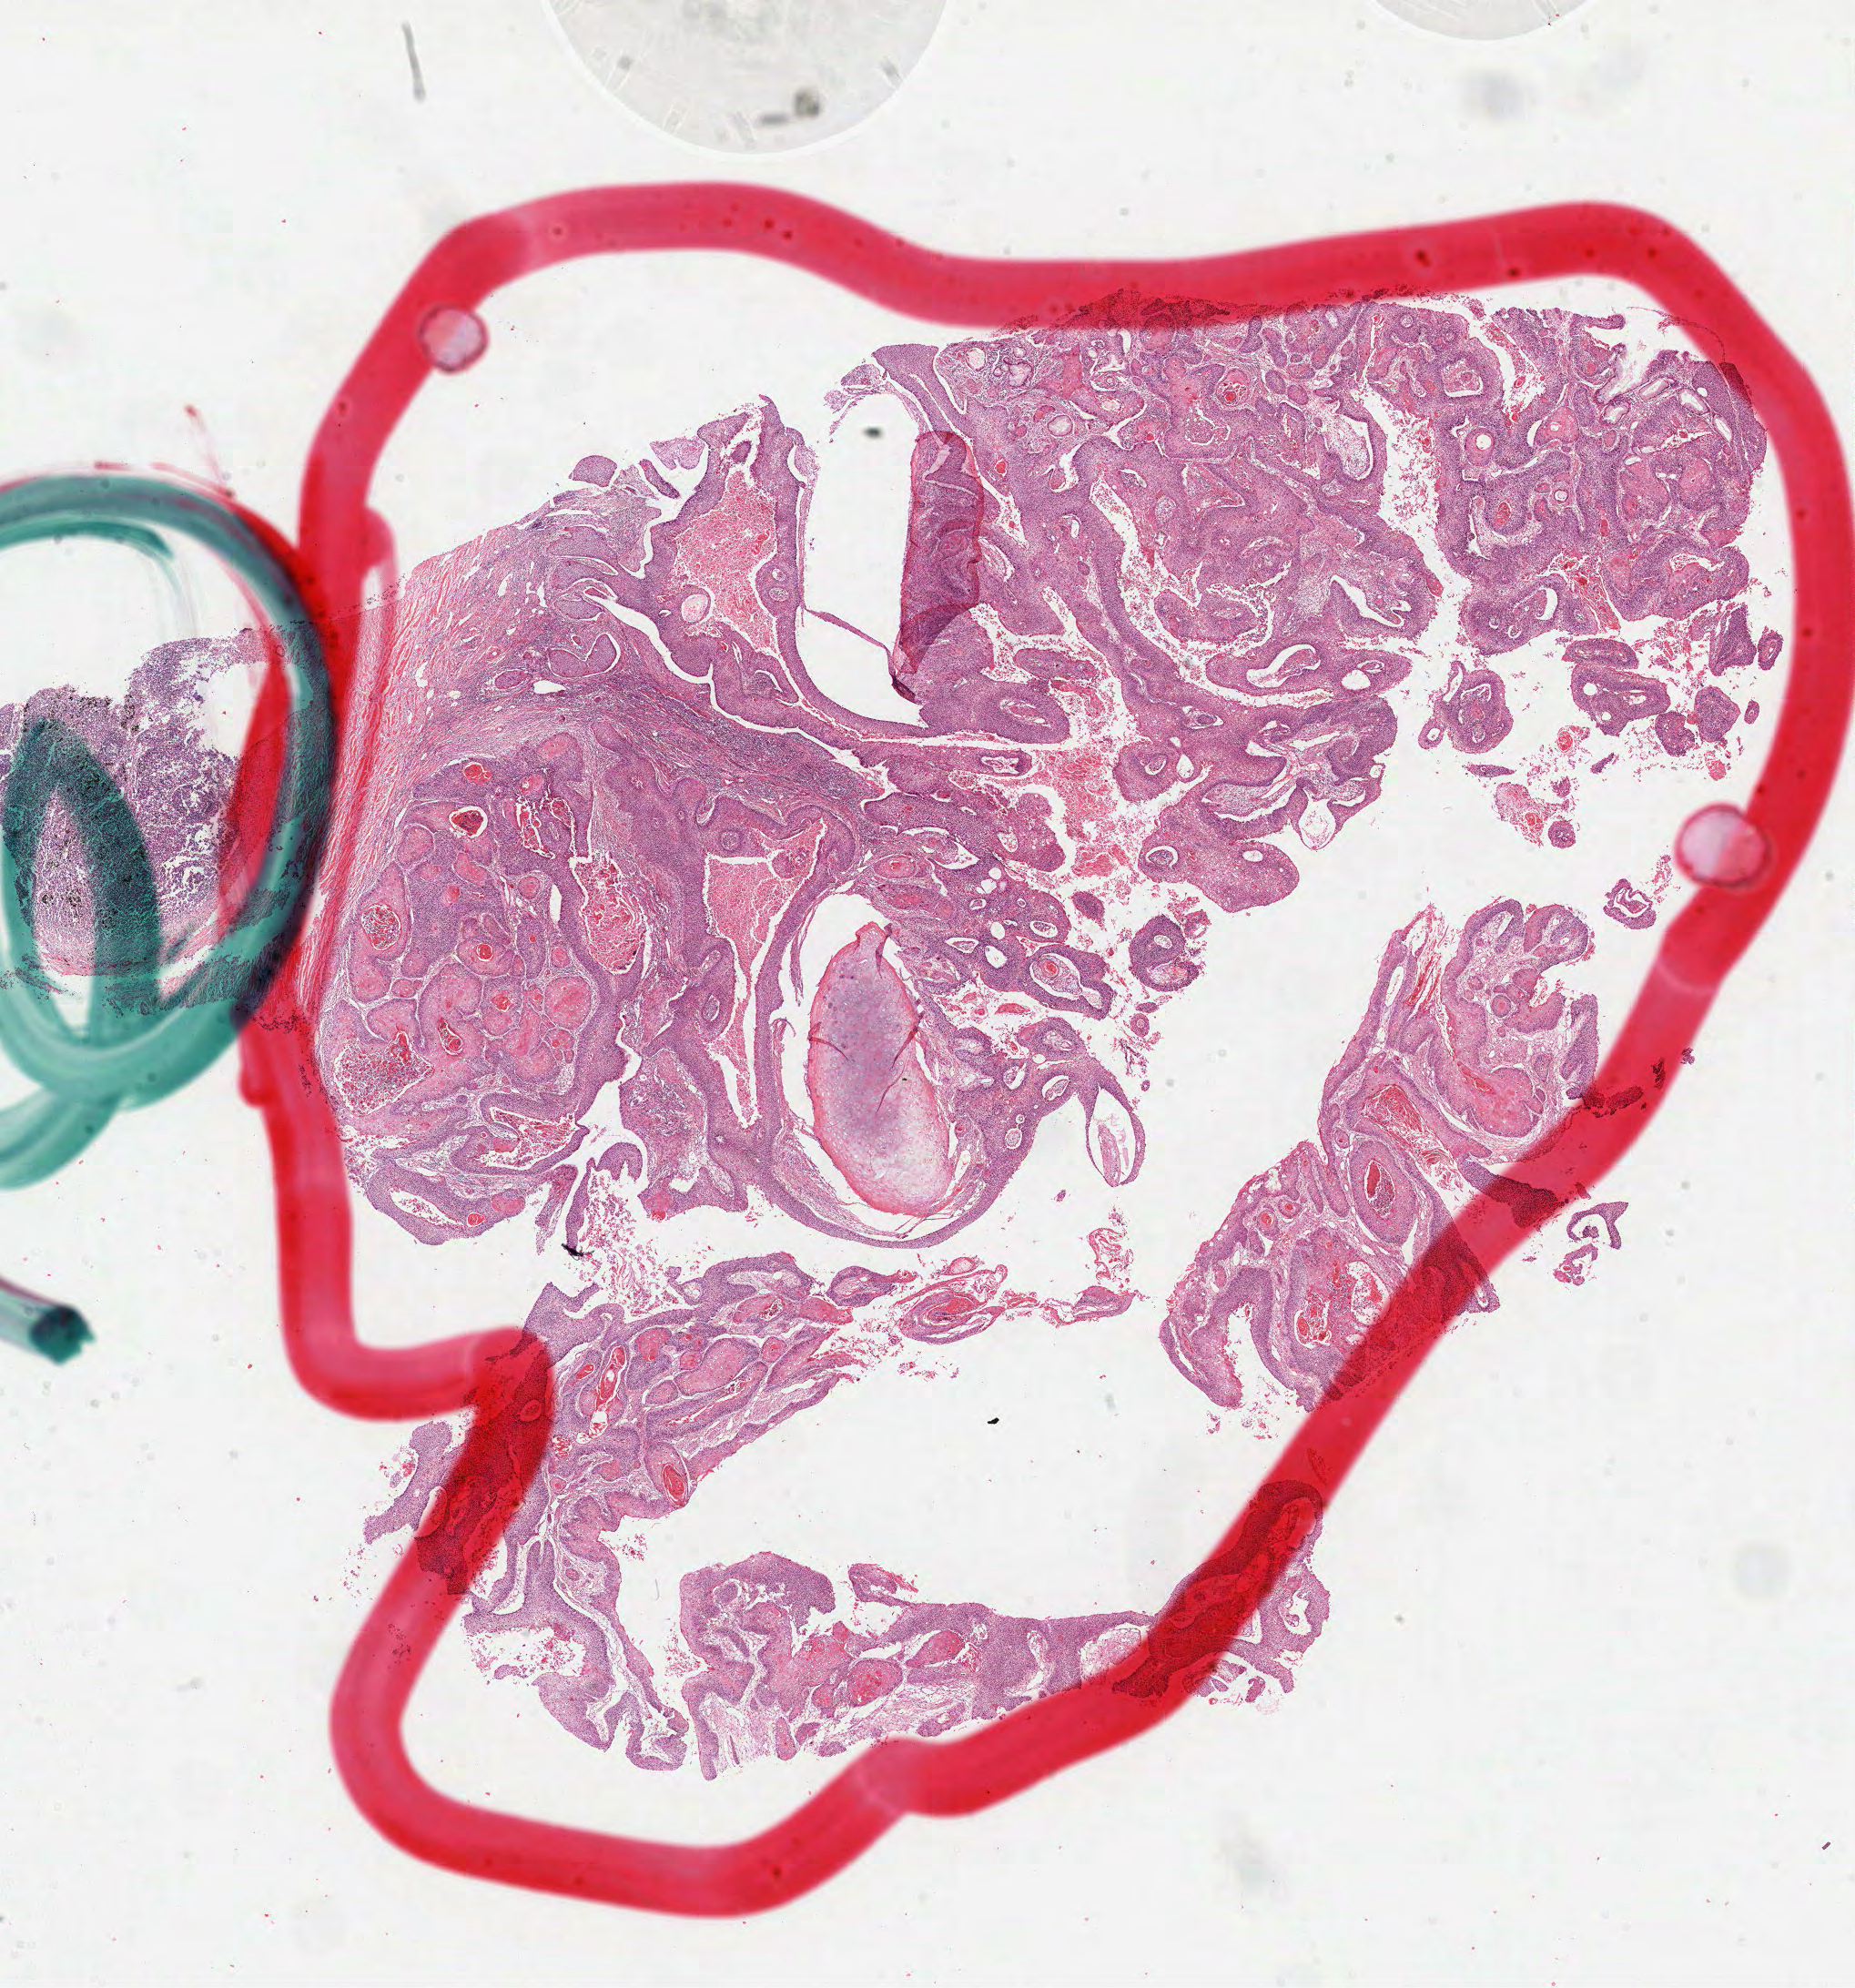
H&E whole-slide image, a low-resolution overview of the entire scanned area, about 16.4 x 17.6 mm. Formalin-fixed paraffin-embedded (FFPE) diagnostic section. Primary tumour sample from the lung. Male, age 49 years at initial diagnosis.
- laterality: left
- histologic diagnosis: Squamous cell carcinoma, NOS
- TNM: T3 N0 M0
- AJCC pathologic stage: IIB (7th edition)